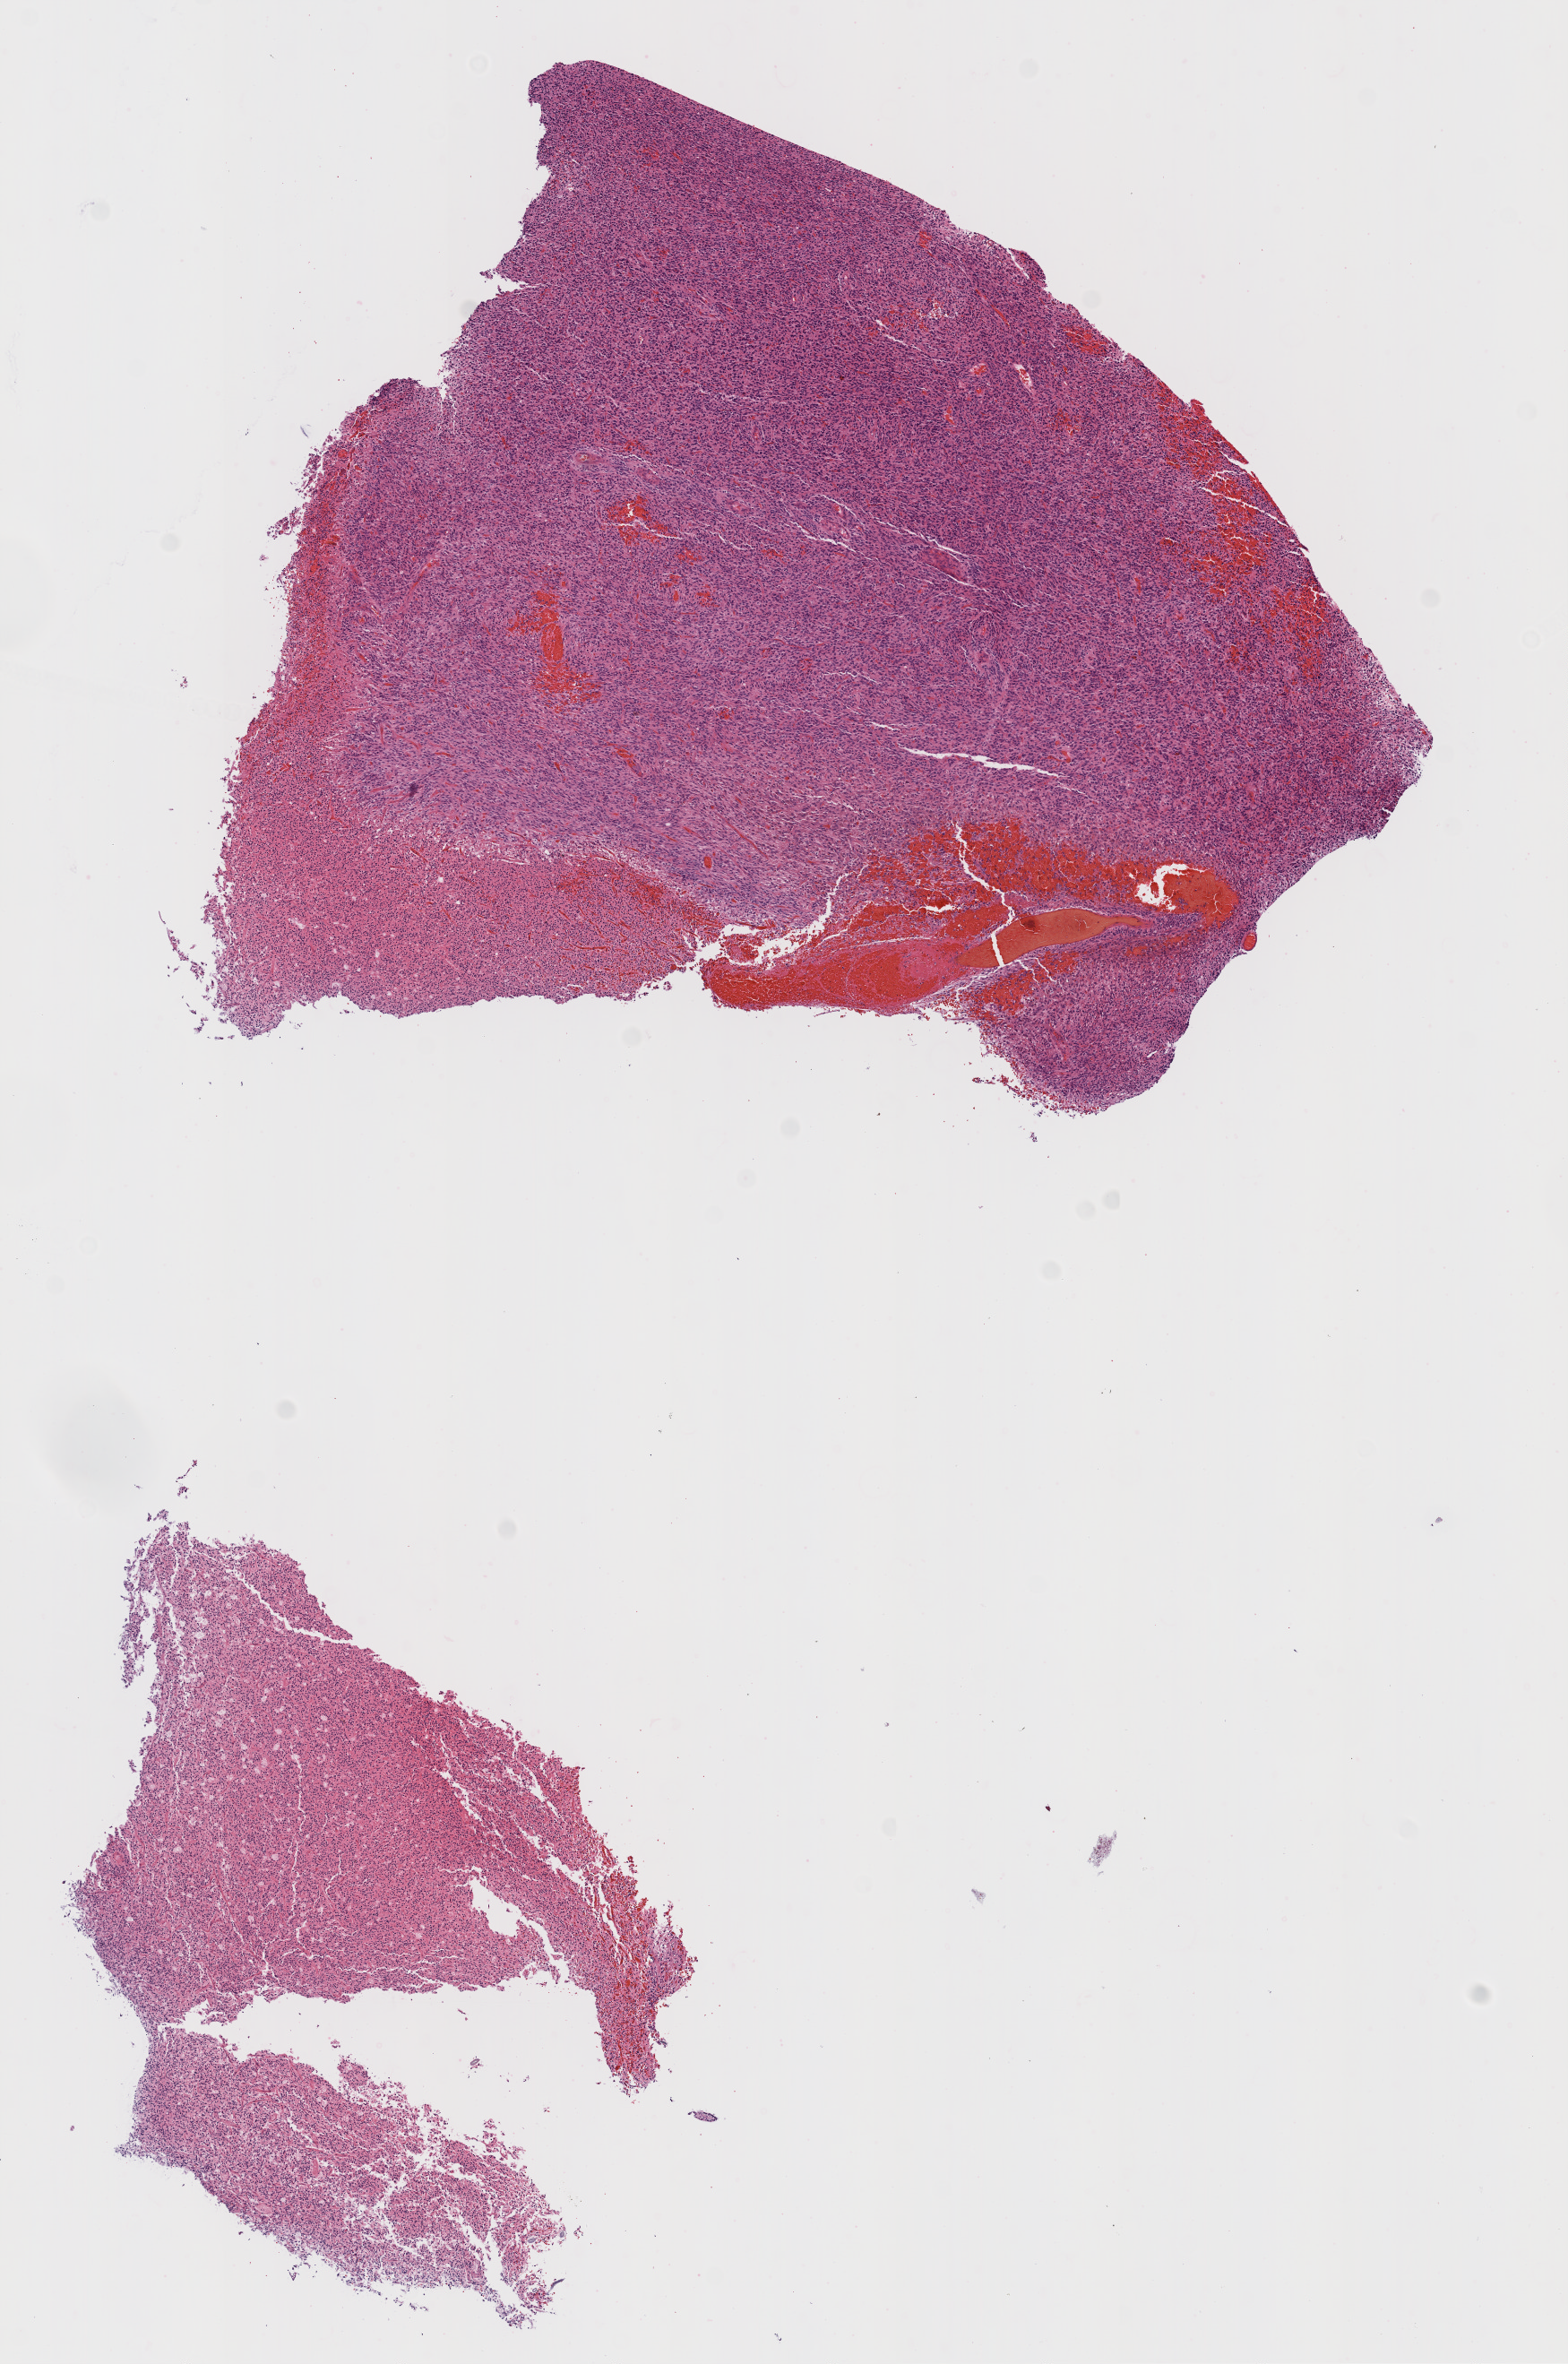
Whole-slide histology image, Hematoxylin and eosin (H&E) stained — low-resolution overview of the scanned area, about 7.0 x 10.6 mm; formalin-fixed paraffin-embedded (FFPE) diagnostic section; brain, primary tumour sample. Patient: female, age at initial diagnosis 53 years.
Pathologic diagnosis: Glioblastoma.